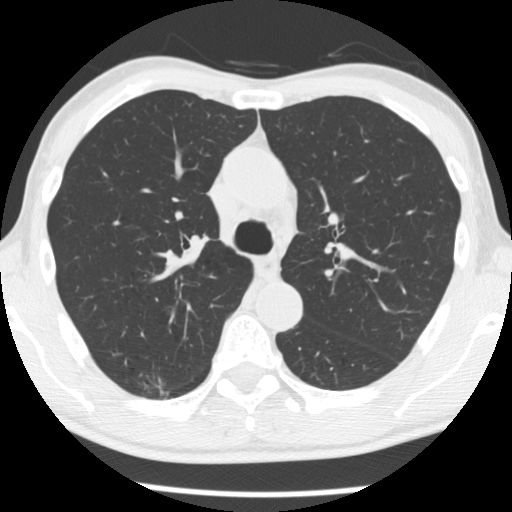
Chest CT (low-dose screening protocol), one axial image; baseline annual screen; lung window (W 1500 / L -600 HU); 2.5 mm slice thickness. Male, age 66 years at enrolment. Former smoker at enrolment.
- Lesion marked by an expert reader, box from (x=127, y=356) to (x=193, y=409) px.
- The screening reader recorded 4 non-calcified nodules or masses ≥4 mm on this exam; which of them this box marks is not recorded.
- Participant outcome: lung cancer diagnosed 503 days after this screen (after the second annual screen) — adenocarcinoma, NOS, right upper lobe, undifferentiated (G4), stage IA (AJCC 6th edition), 20 mm at pathology.